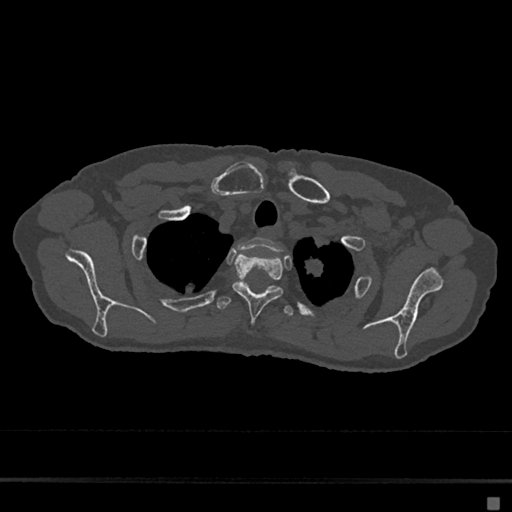
CT including the spine, one axial slice. Slice 570 of 797 in the series (ordered by position). Reconstruction kernel Br40s/3. Bone window (W 1800 / L 400 HU). 0.5 mm slice thickness. 512 × 512 image matrix. Patient: female, 68 years. Case-level facts recorded for this patient, not image findings: primary cancer: renal.
Outlined on this slice (semi-automatic segmentation, software-assisted and operator-edited):
- T1 vertebra: bounding box <238,237,281,252> (left, top, right, bottom; pixels)
- T2 vertebra: <232,254,284,321>
- T3 vertebra: <216,281,294,315>